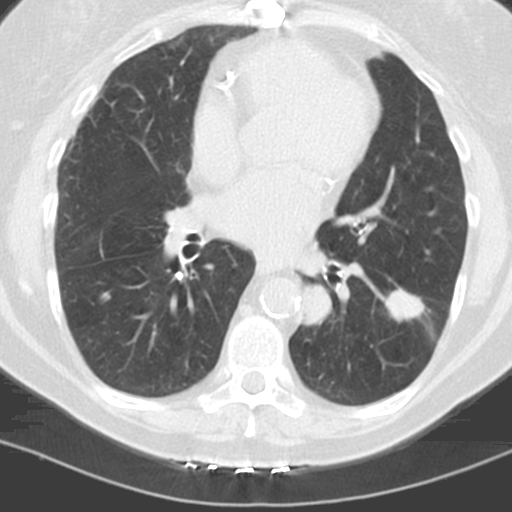
Axial slice from a low-dose chest CT screening exam, baseline screening round, lung window (W 1500 / L -600 HU), standard (soft-tissue) reconstruction kernel (C), 120 kVp, slice 69 of 121 in the series. Female participant, aged 60 years at enrolment. Former smoker at enrolment.
2 expert reader's lesion annotations on this slice (largest first), box from (x=289, y=280) to (x=338, y=332) px; (x=374, y=286)–(x=426, y=331). The screening reader recorded 3 non-calcified nodules or masses ≥4 mm on this exam (left lower lobe, left lower lobe, right middle lobe); which of them these boxes mark is not recorded. Official screen result: positive, change unspecified: nodule(s) >= 4 mm or enlarging nodule(s), mass(es), or other non-specific abnormalities suspicious for lung cancer.